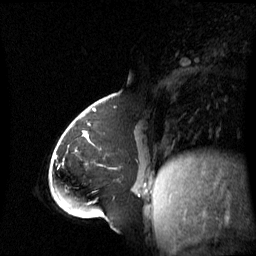
Breast MRI (dynamic contrast-enhanced), one sagittal slice; position 22 of 60 along the scan axis; dynamic contrast-enhanced series, image 2 of 3 at this slice position (ordered by acquisition); 1.5 T; TE 4.2 ms, TR 8.4 ms; 2.8 mm slice thickness; 256 × 256 image matrix, field of view 270 × 270 mm. Patient: female, 43 years. From the clinical record (not read from this slice): setting: breast cancer imaged before/during neoadjuvant chemotherapy; receptor status: triple-negative.
Annotated regions visible in this slice (semi-automatic segmentation, software-assisted and operator-edited):
- analysis volume of interest (the breast-tissue region the enhancement analysis was run in; not a lesion): bounding box (x1, y1, x2, y2) in pixels: (65, 118, 143, 198)
- tumour enhancement mask (voxels above the 70 % enhancement threshold inside the analysis volume of interest): (86, 132, 140, 196)